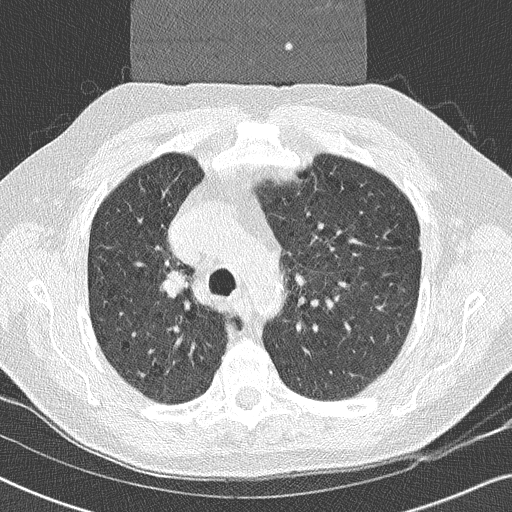
Chest CT (low-dose screening protocol), one axial image, second screening round (one year after baseline), lung window (W 1500 / L -600 HU), slice 80 of 252 in the series. Male participant, aged 59 years at enrolment. Former smoker at enrolment.
- Lesion marked by an expert reader, bounding box <141,256,202,308> (left, top, right, bottom; pixels).
- Screening reader's record for this exam (one nodule recorded; not confirmed to be the boxed lesion): non-calcified nodule or mass ≥4 mm, right upper lobe, 17 × 16 mm, smooth margins, soft tissue attenuation, pre-existing on the prior screen: yes.
- Official screen result: positive, other.
- Later outcome: lung cancer diagnosed 14 days after this screen — squamous cell carcinoma, NOS, right upper lobe, poorly differentiated (G3), stage IIA (AJCC 6th edition), 20 mm at pathology.